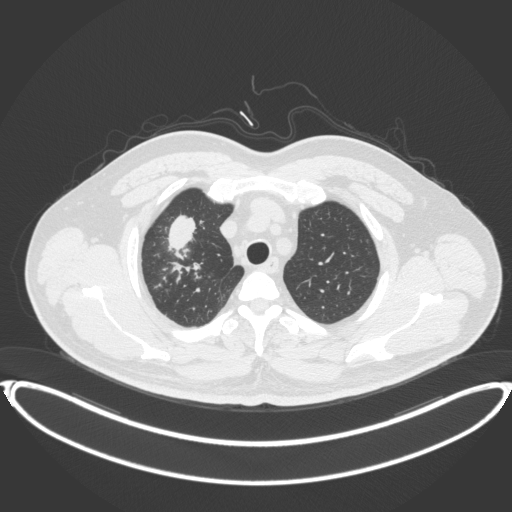
Chest CT, one axial slice. Slice 319 of 399 in the series (ordered by position). Lung window (W 1500 / L -600 HU). 1 mm slice thickness. 512 × 512 image matrix, field of view 445 × 445 mm. Patient: male, 53 years. From the clinical record (not read from this slice): clinical TNM (as recorded): T2a N0 M0.
Structures marked on this image (bounding box drawn by a radiologist):
- lung tumour (recorded histology: adenocarcinoma): bounding box [x1, y1, x2, y2] px = [167, 212, 200, 258]